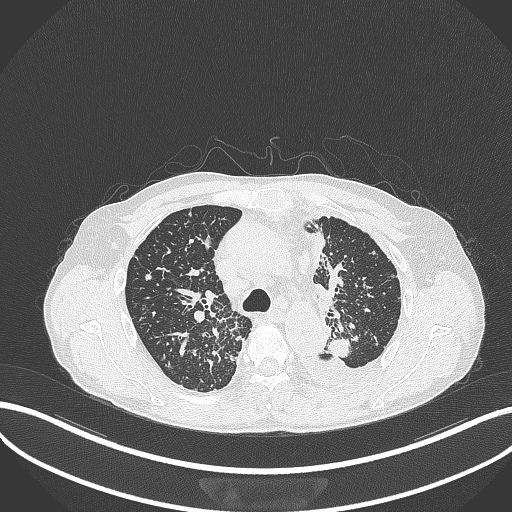
Chest CT, one axial slice; position 252 of 325 along the scan axis; reconstruction kernel B70f; 120 kVp; lung window (W 1500 / L -600 HU); 1 mm slice thickness; 512 × 512 image matrix. Male patient, age 58 years. From the clinical record (not read from this slice): clinical TNM (as recorded): T1c N3 M1.
Outlined on this slice (rectangle marked by the reading radiologist):
- lung tumour (recorded histology: adenocarcinoma): bounding box (x1, y1, x2, y2) in pixels: (323, 335, 355, 360)